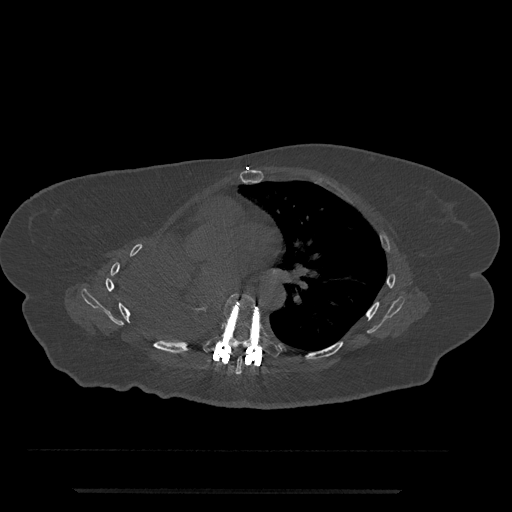
CT including the spine, one axial slice; position 456 of 797 along the scan axis; bone window (W 1800 / L 400 HU); 512 × 512 image matrix, field of view 440 × 440 mm. Female patient, age 51 years. Case-level facts recorded for this patient, not image findings: primary cancer: neuro.
Outlined on this slice (semi-automatic segmentation, software-assisted and operator-edited):
- T6 vertebra: box from (x=235, y=357) to (x=243, y=375) px
- T7 vertebra: (x=203, y=293)–(x=281, y=358)